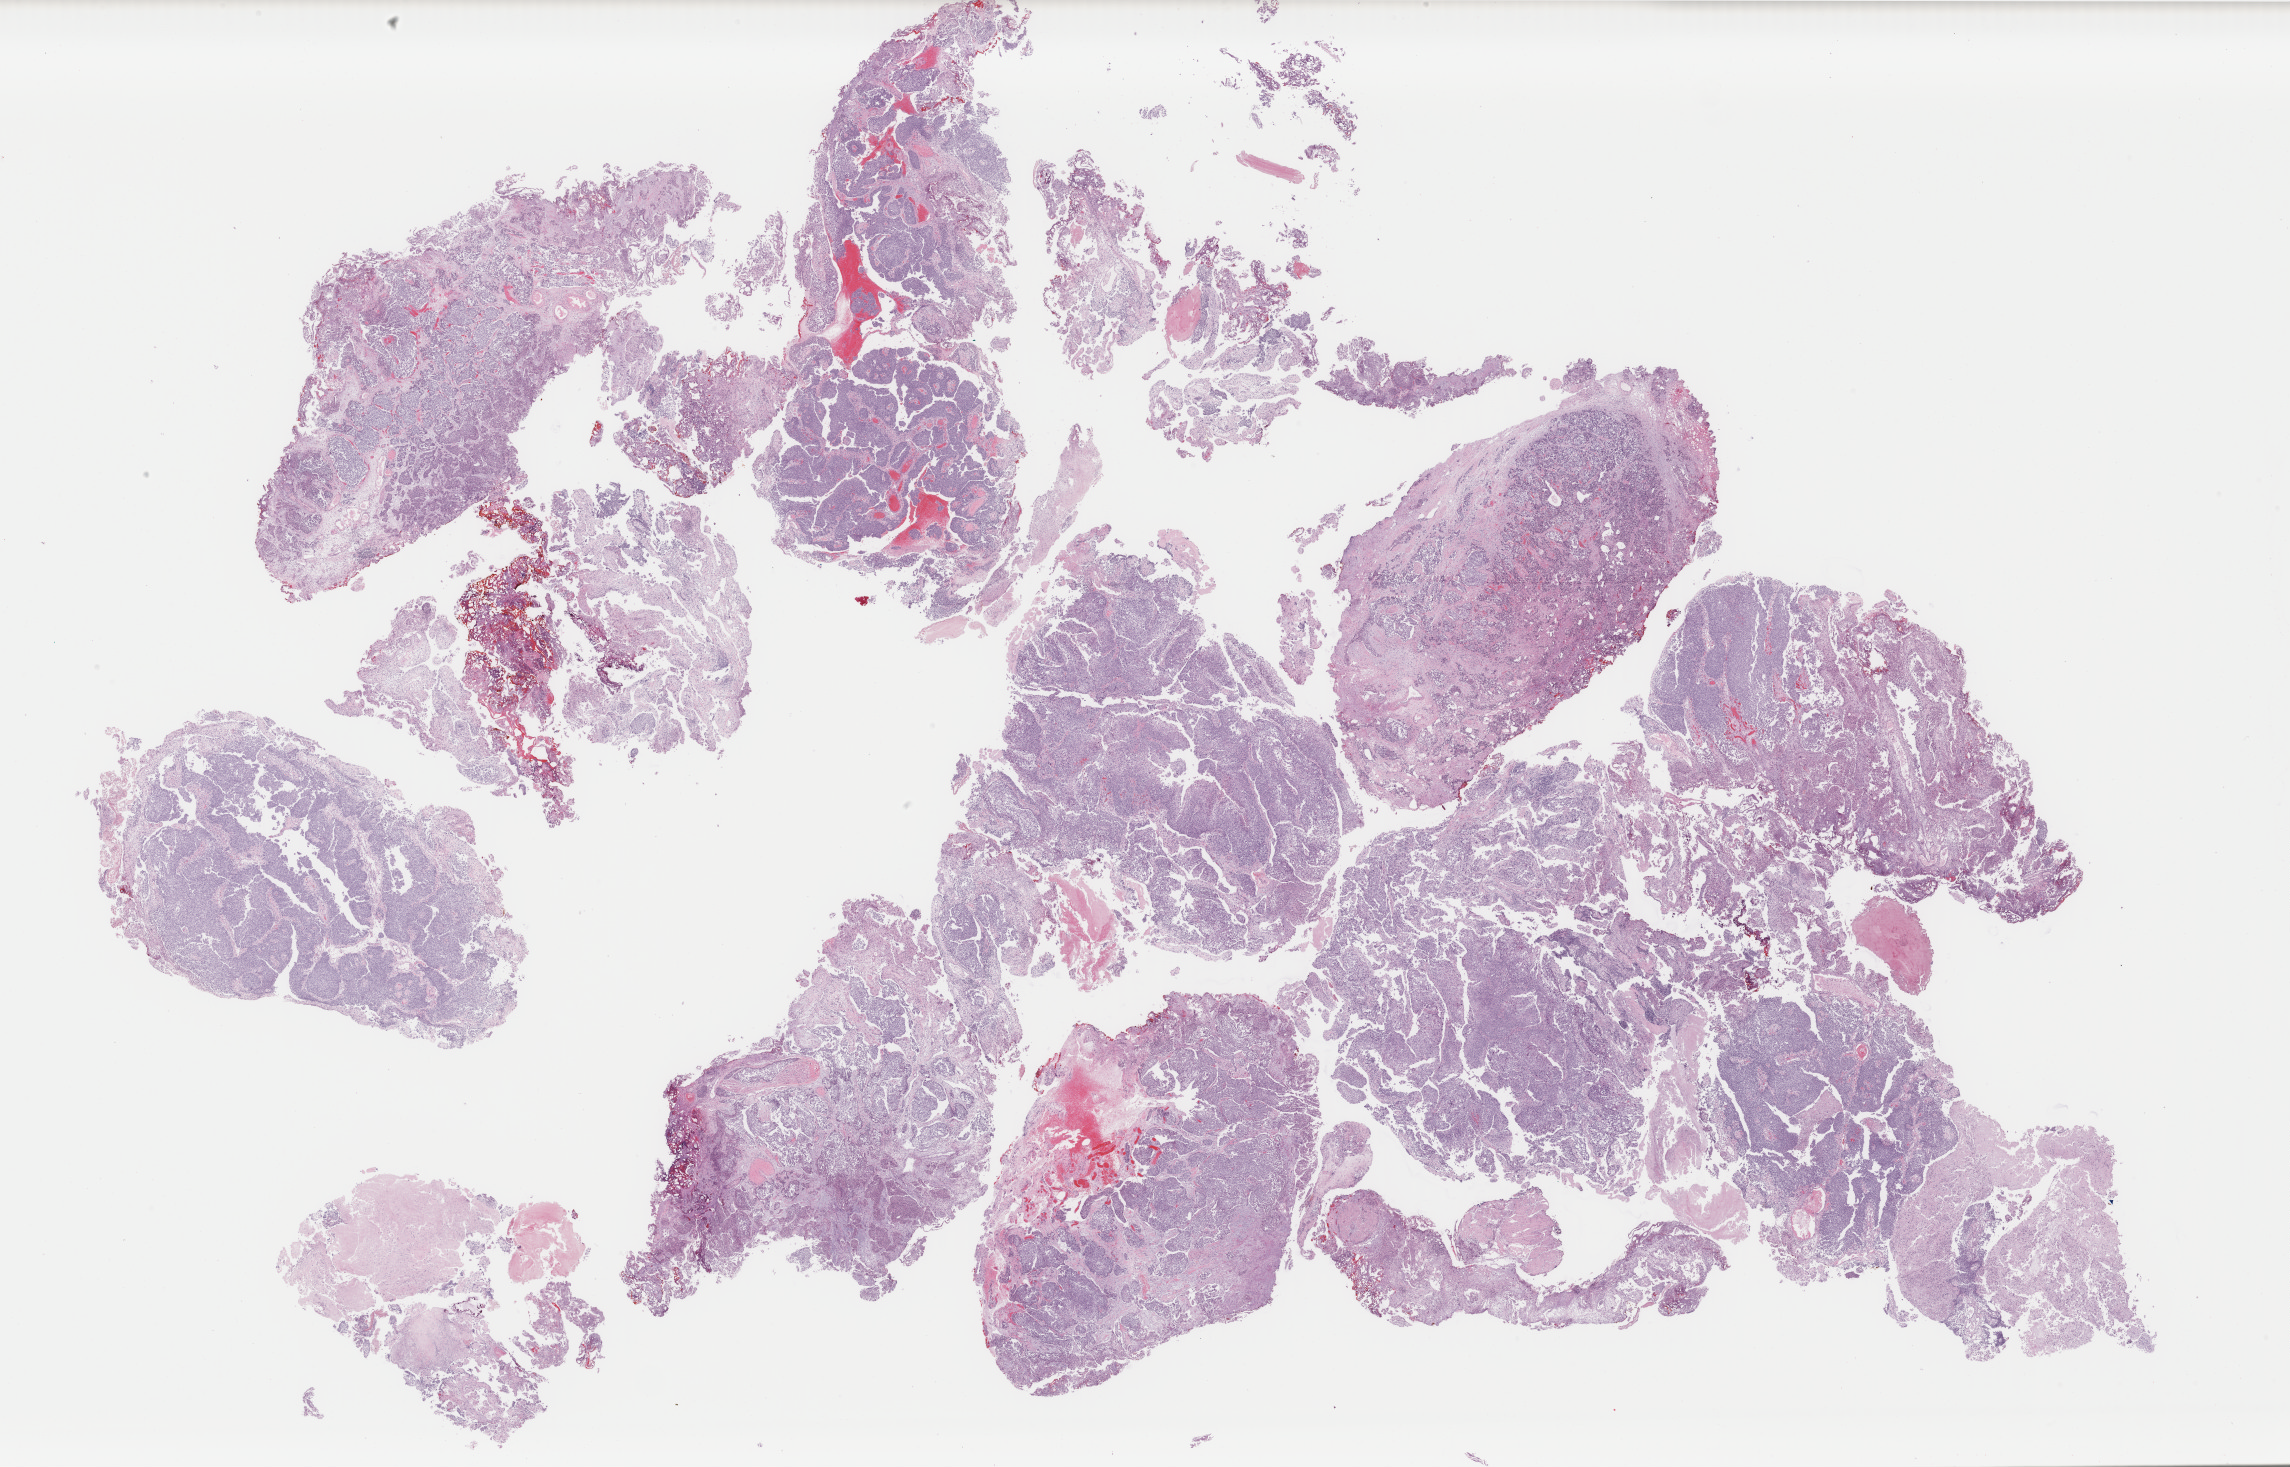
Digitized Hematoxylin and eosin (H&E) stained tissue section (whole slide), whole scanned area (about 36.4 x 23.3 mm, from a 40x scan) shown as a low-resolution overview. FFPE section. Sample: primary tumour, bladder. Patient: male, age at initial diagnosis 68 years. Histologic grade: high grade.
AJCC pathologic stage: IV. TNM: T4a N2 MX. Lymph nodes positive (case pathology): 2 of 10 examined. Histologic diagnosis: Transitional cell carcinoma.